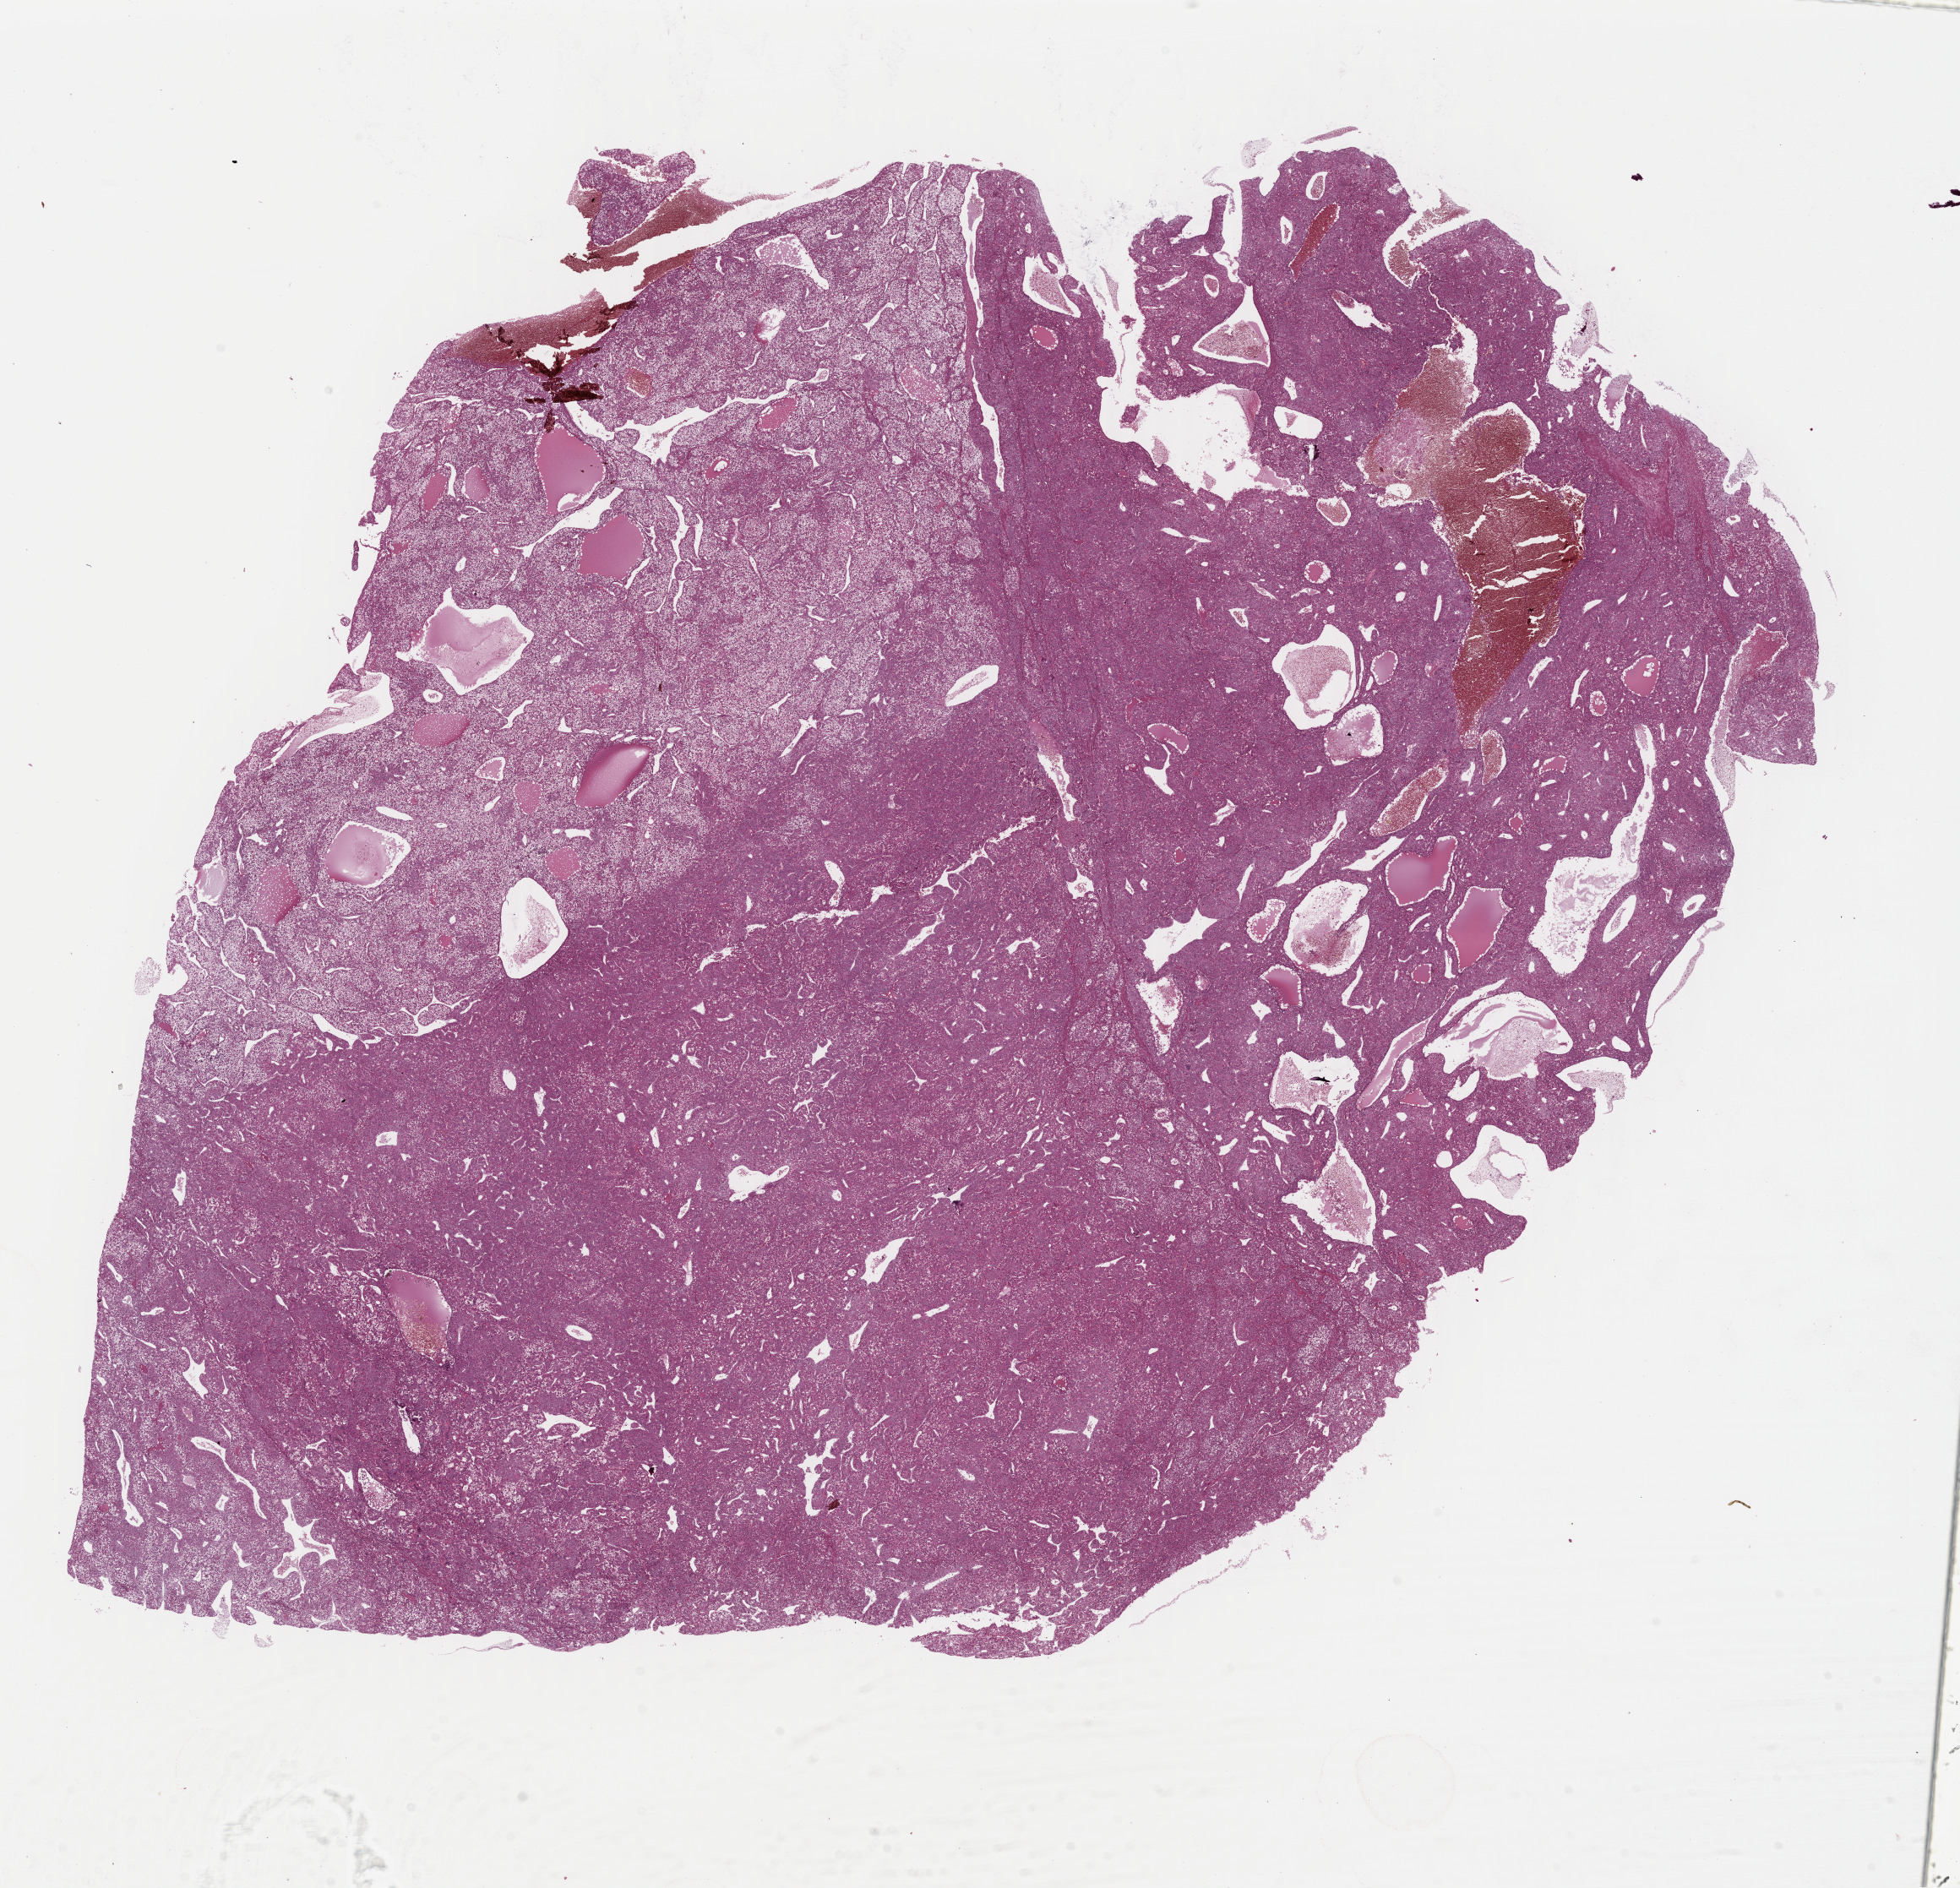
Whole-slide histology image, H&E — shown as a low-resolution overview of the whole scanned area (about 18.2 x 17.6 mm, acquisition: 40x scan). FFPE section. Sample: primary tumour, liver. Male, age 48 years at initial diagnosis. Histologic grade: G2 (moderately differentiated).
* histologic diagnosis: Hepatocellular carcinoma, NOS
* AJCC pathologic stage: IIIB (6th edition)